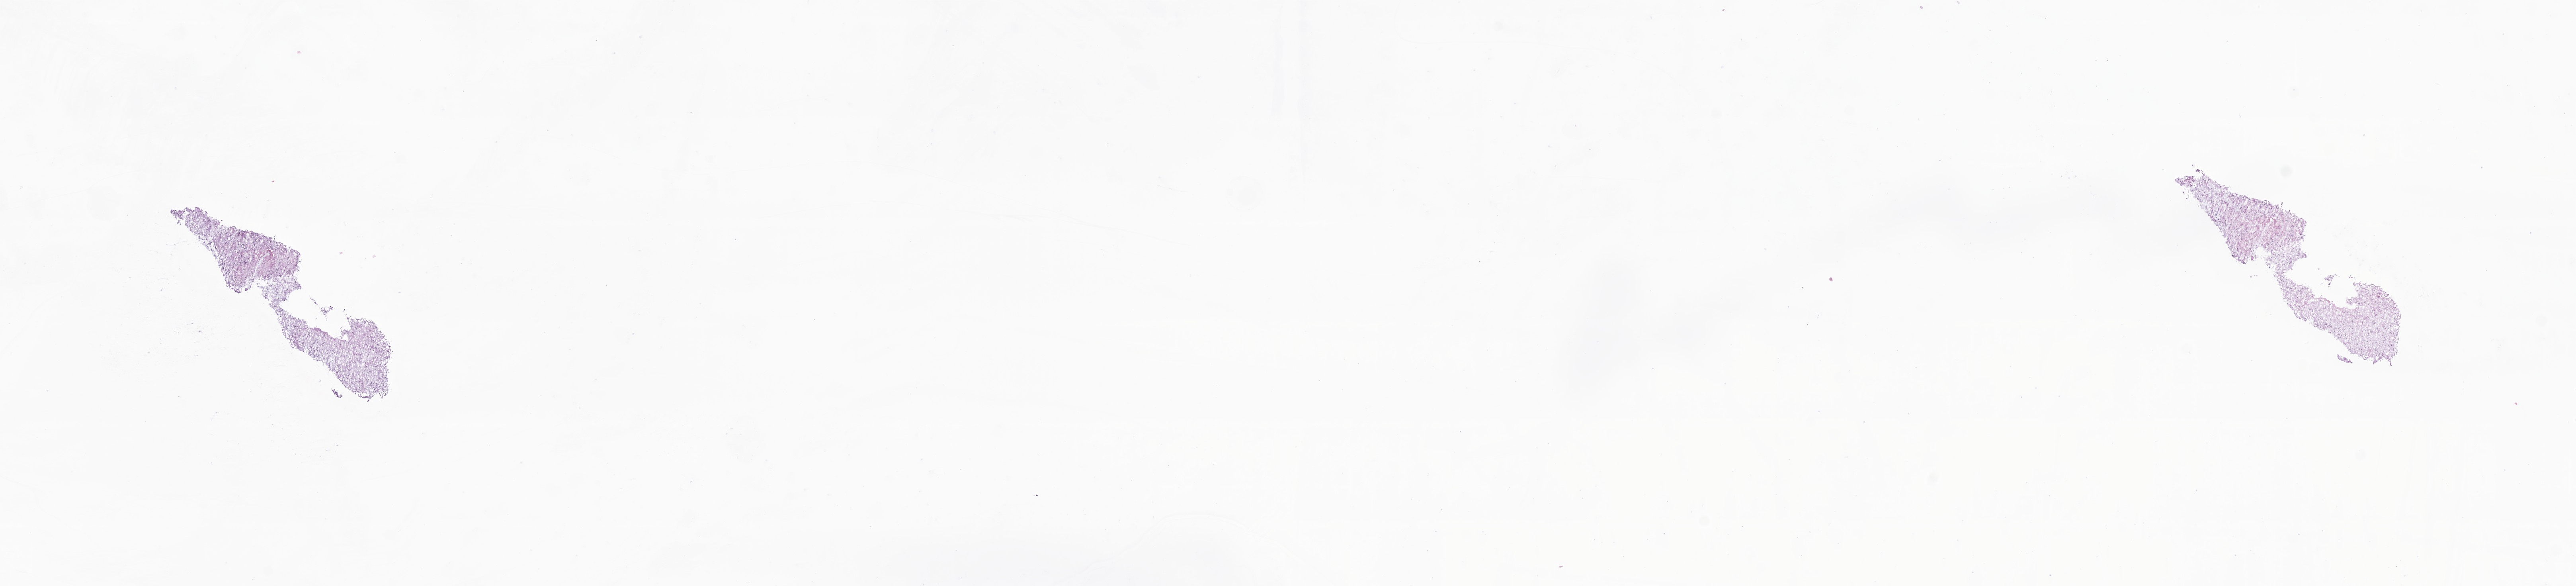
Haematoxylin and eosin whole-slide image of tumor tissue from the brain — a low-resolution overview of the entire scanned area, about 27.3 x 6.2 mm; frozen section. Male patient, age 930 days (about 2.5 years).
Diagnosis (ICD-O-3 morphology term): Pilocytic astrocytoma.